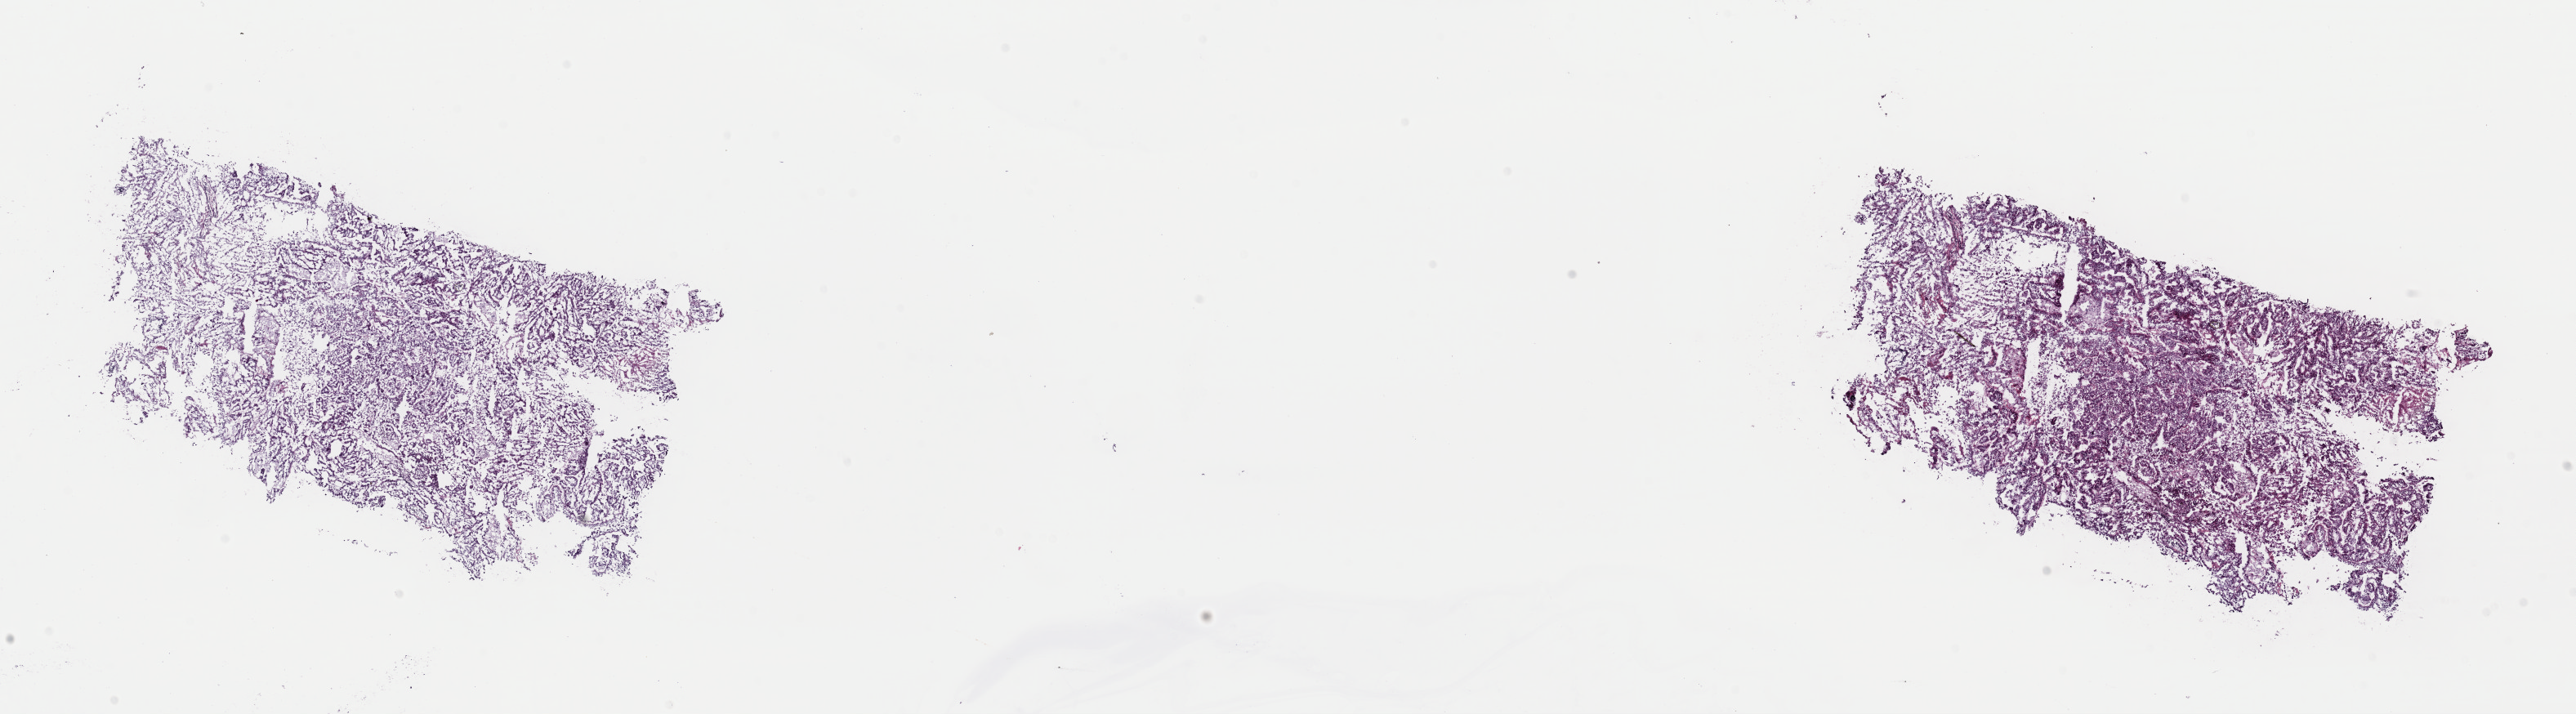
Whole-slide histology image, Hematoxylin and eosin (H&E) stained, a low-resolution overview of the entire scanned area, about 24.9 x 6.9 mm (acquisition: 40x scan), frozen section from the top of the tissue portion, primary tumour sample from the kidney. Patient: male, age at initial diagnosis 67 years. Composition of this section per pathologist review: tumour cells 70%, tumour nuclei 70%, normal cells 0%, stromal cells 30%, necrosis 0%. Inflammatory infiltration, as recorded: lymphocyte infiltration 0%, monocyte infiltration 100%, neutrophil infiltration 0%.
• diagnosis: Papillary adenocarcinoma, NOS
• AJCC pathologic stage: III
• lymph nodes positive (case pathology): 1 of 3 examined
• laterality: left